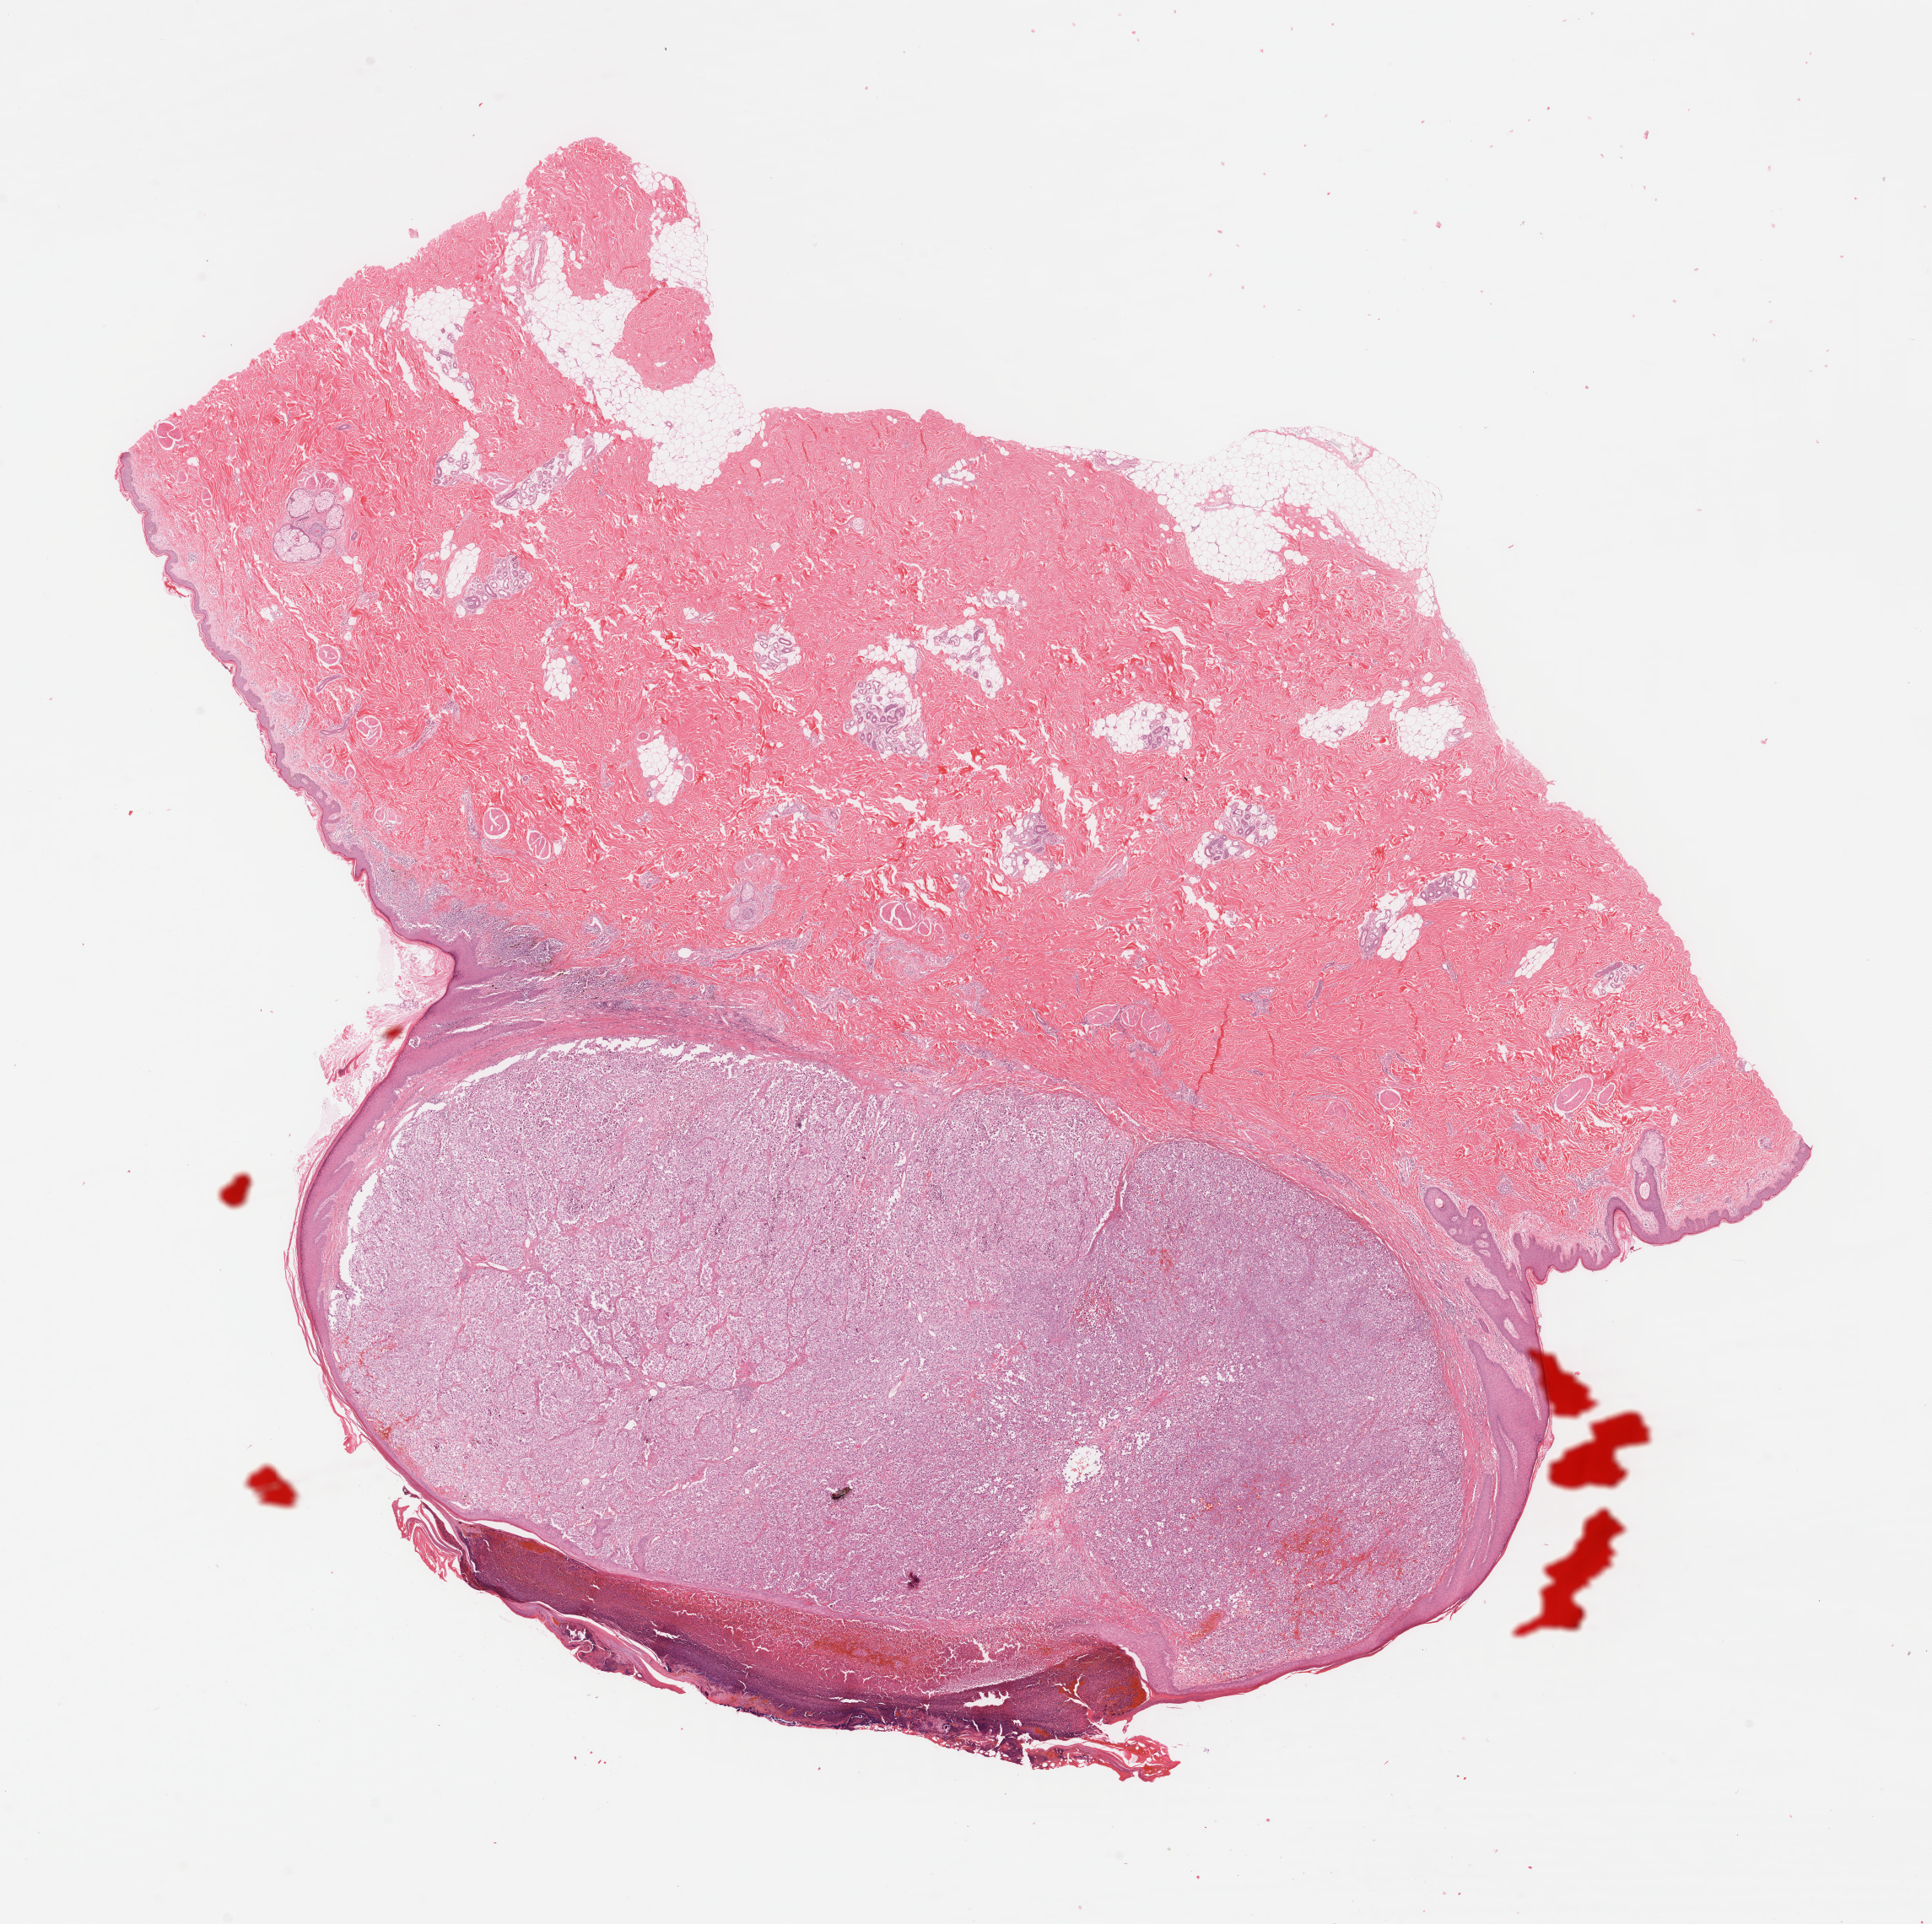
Digitized H&E-stained tissue section (whole slide), low-resolution overview of the scanned area, about 18.0 x 17.9 mm (slide scanned at 40x); formalin-fixed paraffin-embedded (FFPE) diagnostic section; primary tumour sample from the skin. Male, age 69 years at initial diagnosis.
Diagnosis: Malignant melanoma, NOS. AJCC pathologic stage: IIB.